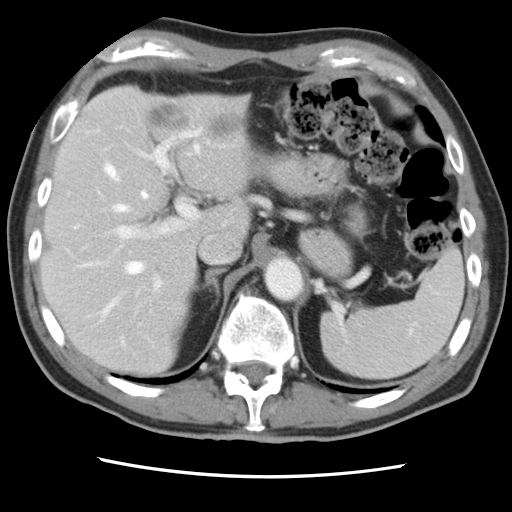
Contrast-enhanced abdominal CT, one axial slice. Position 58 of 83 along the scan axis. Intravenous contrast given. Soft-tissue window (W 400 / L 40 HU). 5 mm slice thickness. 512 × 512 image matrix. Male patient, age 69 years. Case-level facts recorded for this patient, not image findings: diagnosis: colorectal cancer liver metastases, imaged before liver resection.
Structures marked on this image (manually delineated by an expert):
- hepatic veins: bounding box [x1, y1, x2, y2] px = [76, 145, 199, 342]
- liver: [42, 86, 250, 376]
- planned liver remnant (the part of the liver to remain after resection): [42, 142, 206, 375]
- portal vein (with intrahepatic branches): [112, 125, 227, 292]
- liver metastasis: [150, 104, 188, 127]
- liver metastasis: [211, 116, 243, 136]